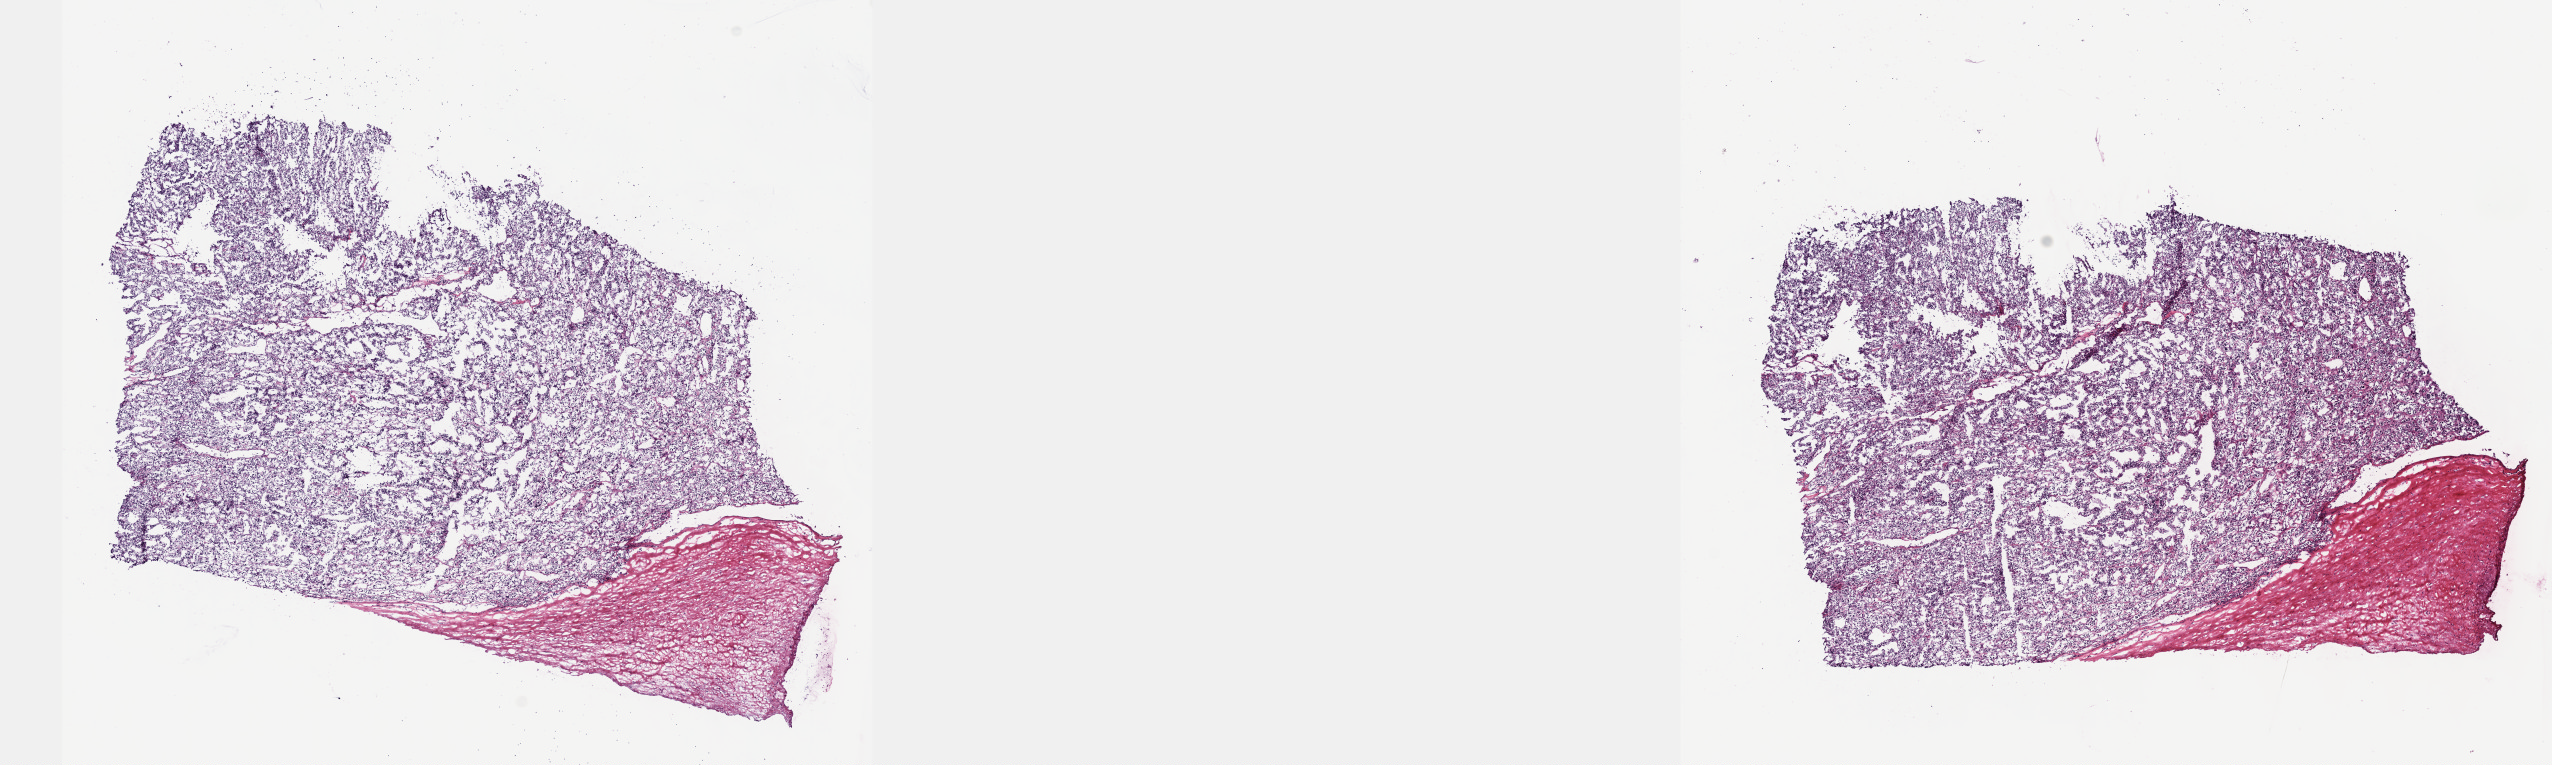
H&E whole-slide image, a low-resolution overview of the entire scanned area, about 20.6 x 6.2 mm. Frozen section from the top of the tissue portion. Kidney, primary tumour sample. Patient: female, age at initial diagnosis 62 years.
Pathologic diagnosis: Clear cell adenocarcinoma, NOS.